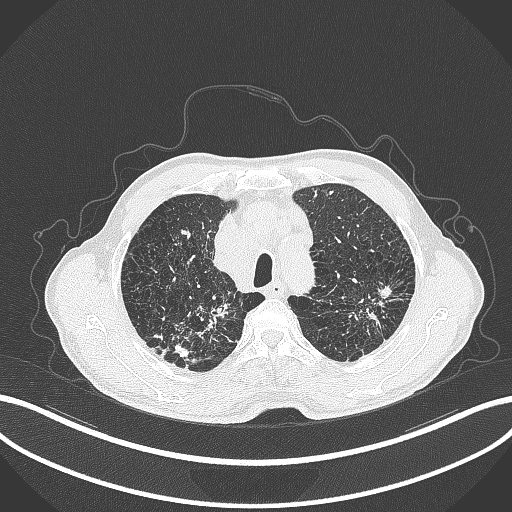
Chest CT, one axial slice; slice 360 of 463 in the series (ordered by position); reconstruction kernel B70f; lung window (W 1500 / L -600 HU); 512 × 512 image matrix, field of view 400 × 400 mm. Patient: male, 74 years. From the clinical record (not read from this slice): clinical TNM (as recorded): T2a N1 M0.
Annotated regions visible in this slice (bounding box drawn by a radiologist):
- lung tumour (recorded histology: adenocarcinoma): bounding box (x1, y1, x2, y2) in pixels: (352, 286, 394, 333)